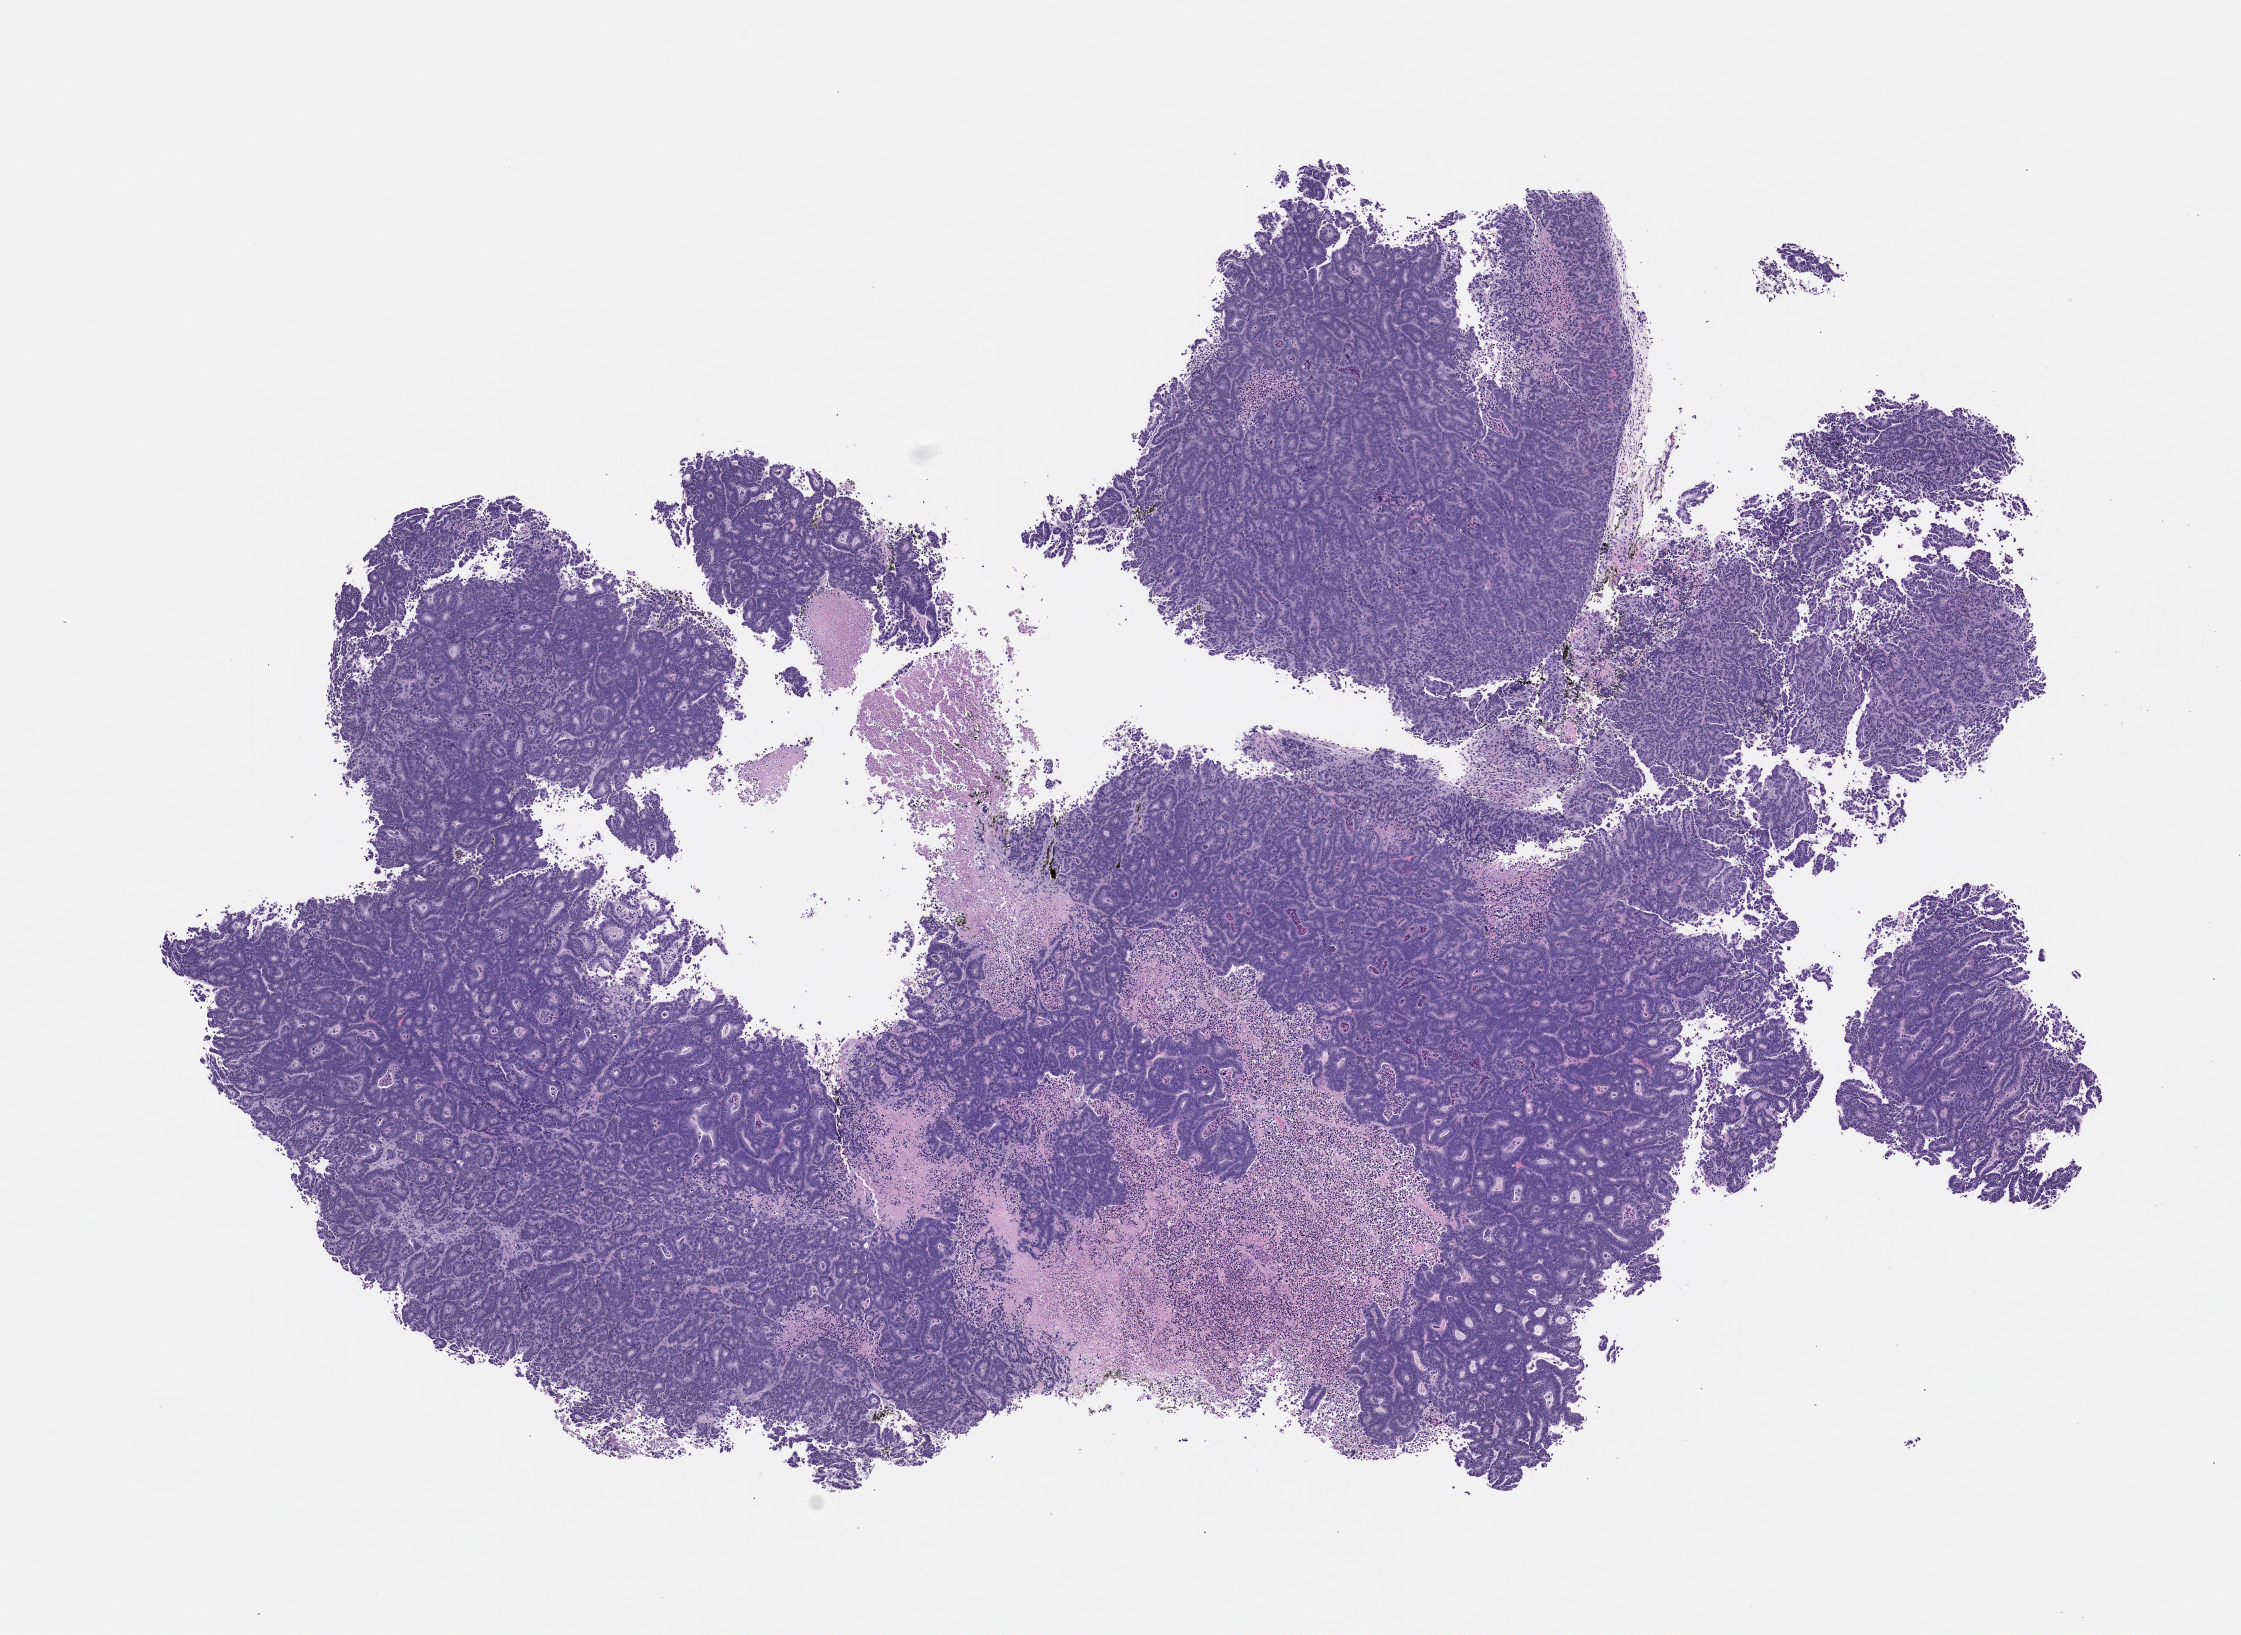
H&E whole-slide image of a patient-derived xenograft (PDX) tumor grown in a mouse — a low-resolution overview of the entire scanned area, about 9.0 x 6.6 mm, FFPE section, tumor site category: small intestine.
* originating patient diagnosis: Small Intestinal Adenocarcinoma